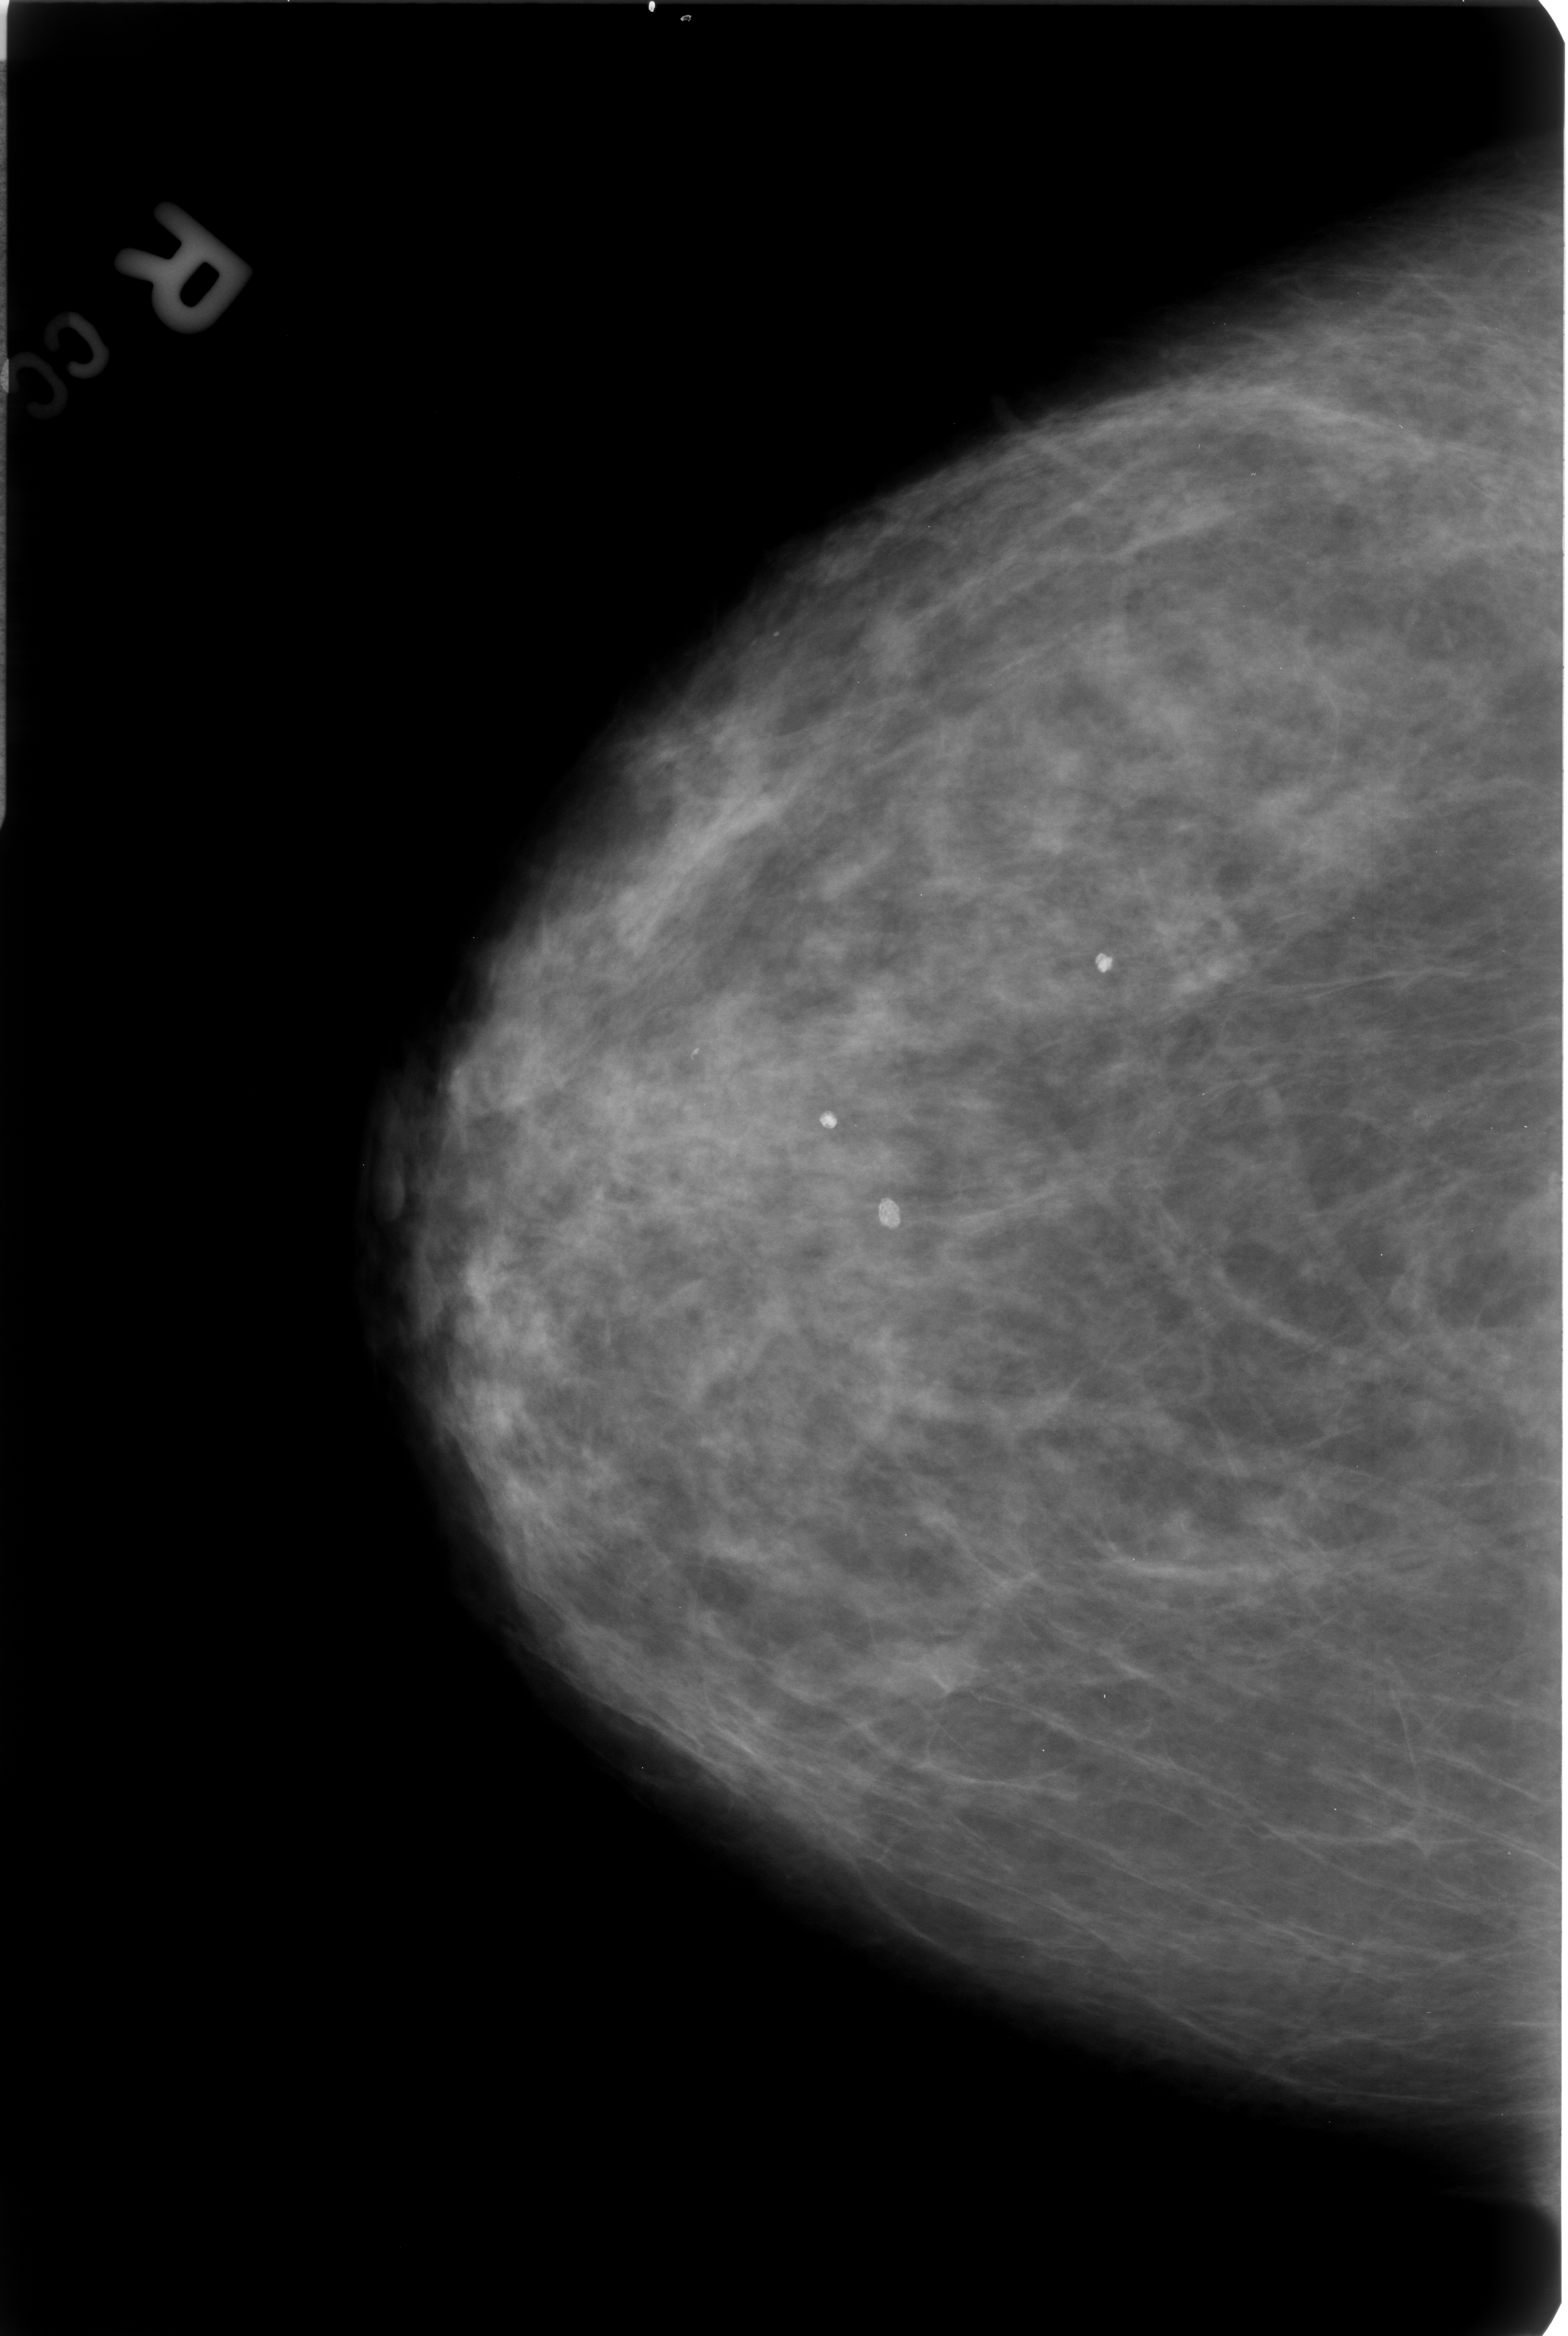
Digitized screen-film mammogram, right breast, CC view, BI-RADS breast density category 2 (scale 1–4).
- Marked findings (only marked abnormalities are described; nothing is implied about the rest of the image): Finding 1 of 3: calcifications, morphology coarse / round and regular / lucent center; BI-RADS assessment category 2; subtlety rating 4 on a 1 (subtle) to 5 (obvious) scale; benign; no additional work-up was recommended (benign without callback).
- Finding 2 of 3: calcifications, morphology coarse / round and regular / lucent center; BI-RADS assessment category 2; benign without callback (not worked up further).
- Finding 3 of 3: calcifications, morphology coarse / round and regular / lucent center; BI-RADS assessment category 2; subtlety rating 5 on a 1 (subtle) to 5 (obvious) scale; benign without callback (not worked up further).